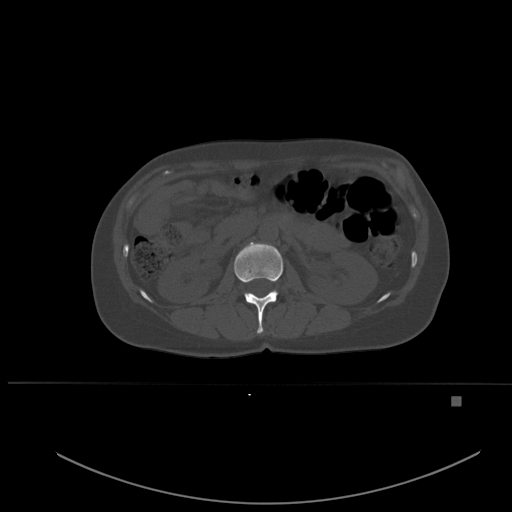
CT including the spine, one axial slice; bone window (W 1800 / L 400 HU); 1.5 mm slice thickness; 512 × 512 image matrix. Patient: female, 49 years. Case-level facts recorded for this patient, not image findings: primary cancer: breast.
Annotated regions visible in this slice (semi-automatic segmentation, software-assisted and operator-edited):
- L1 vertebra: bounding box (x1, y1, x2, y2) in pixels: (234, 242, 283, 334)